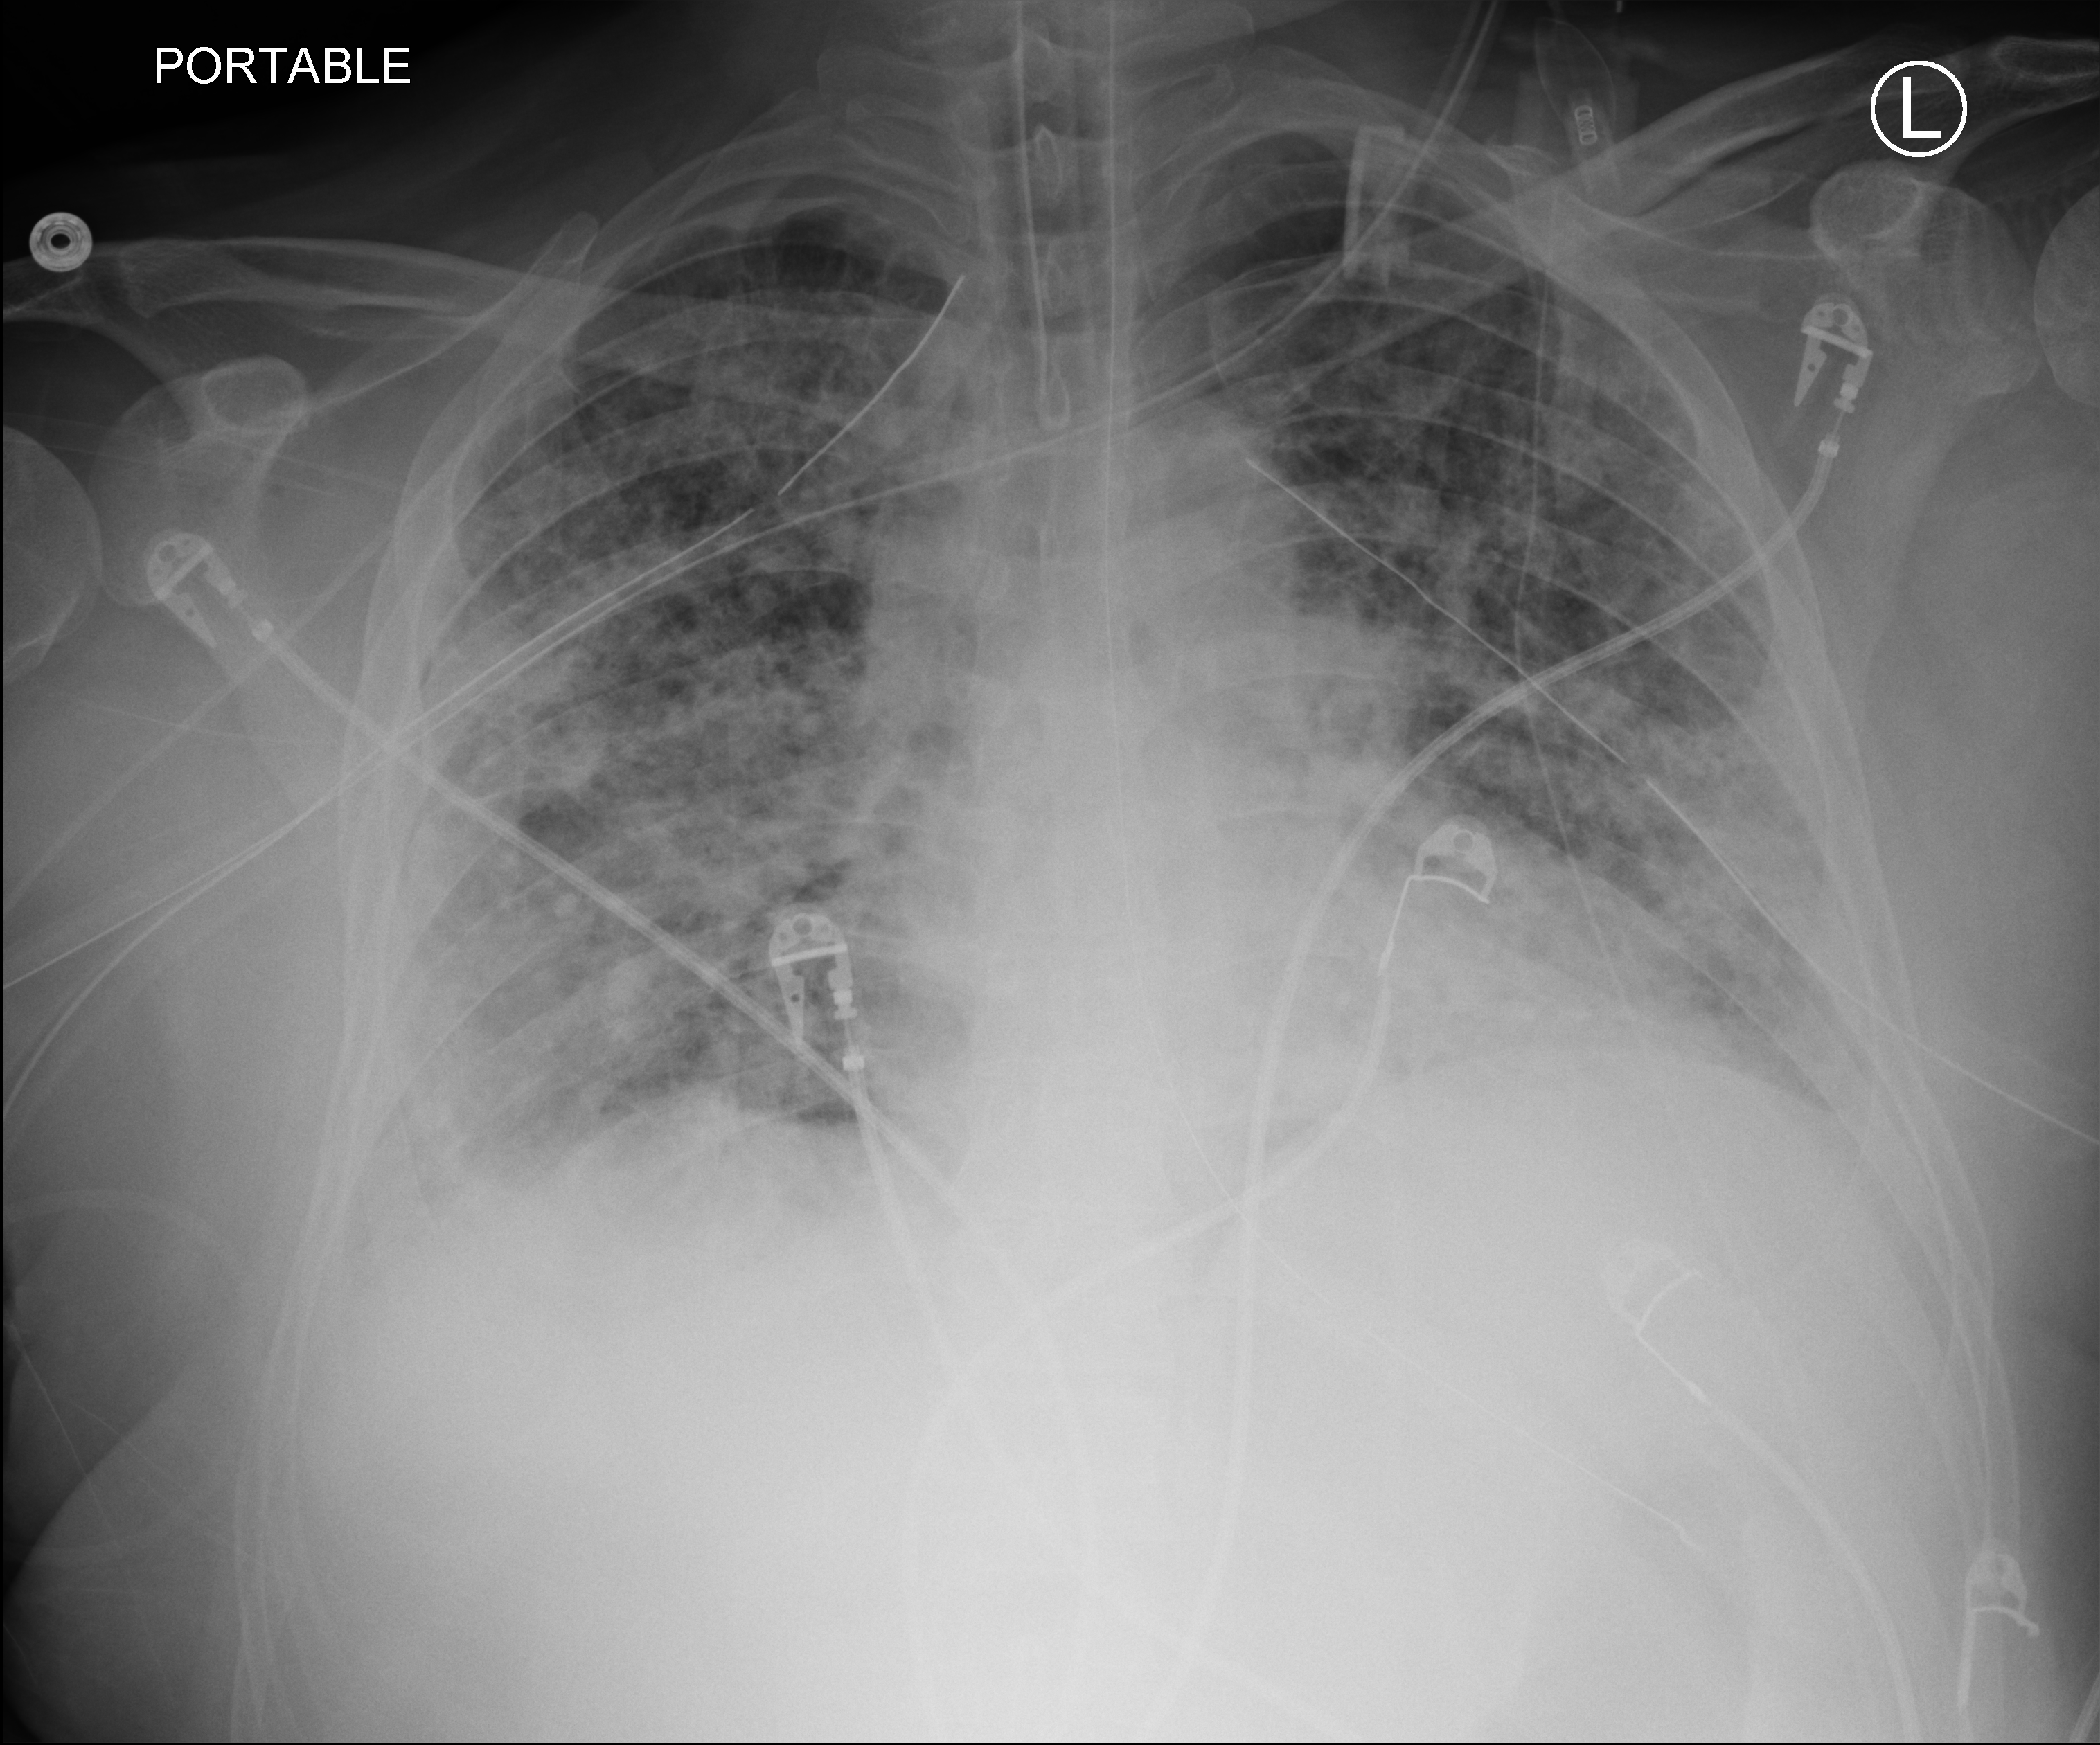
Chest X-ray (portable), anteroposterior (AP) projection. Patient hospitalised with COVID-19; male, aged 18–59 years.
Hospital-stay facts (about this admission, not read from this image; timing relative to this image not recorded):
- mechanically ventilated during this hospital stay: yes
- admitted to intensive care during this hospital stay: yes
- smoking status (admission record): never